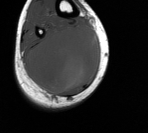
MRI of an extremity soft-tissue mass, one axial slice; MR volume resampled by the dataset authors to the PET/CT grid (not the native acquisition matrix); 3.27 mm slice thickness; 148 × 133 image matrix. Male patient. Case-level facts recorded for this patient, not image findings: histological type: liposarcoma - round cell; grade: high; site of the primary tumour: right calf.
Outlined on this slice (expert contour drawn on MRI and transferred to this co-registered scan by the dataset authors):
- gross tumour volume (mass): box from (x=26, y=25) to (x=101, y=93) px